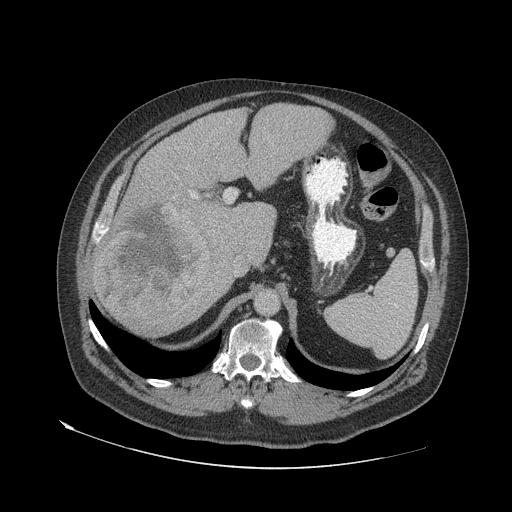
Contrast-enhanced abdominal CT (liver protocol), one axial slice. Position 42 of 79 along the scan axis. 140 kVp. Soft-tissue window (W 400 / L 40 HU). 2.5 mm slice thickness. 512 × 512 image matrix, field of view 480 × 480 mm. From the clinical record (not read from this slice): diagnosis: hepatocellular carcinoma (patient treated with transarterial chemoembolisation; whether this scan precedes or follows treatment is not stated here); TNM stage (as recorded): Stage-IVA; Child-Pugh class: A; tumour differentiation: well differentiated; tumour nodularity: multinodular.
Structures marked on this image (semi-automatically segmented with operator editing):
- liver parenchyma outside the tumour (the mass and vessels are separate outlines, so this box may not span the whole liver): bounding box (x1, y1, x2, y2) in pixels: (92, 104, 331, 334)
- mass: (96, 201, 213, 319)
- liver vessels: (93, 192, 197, 242)